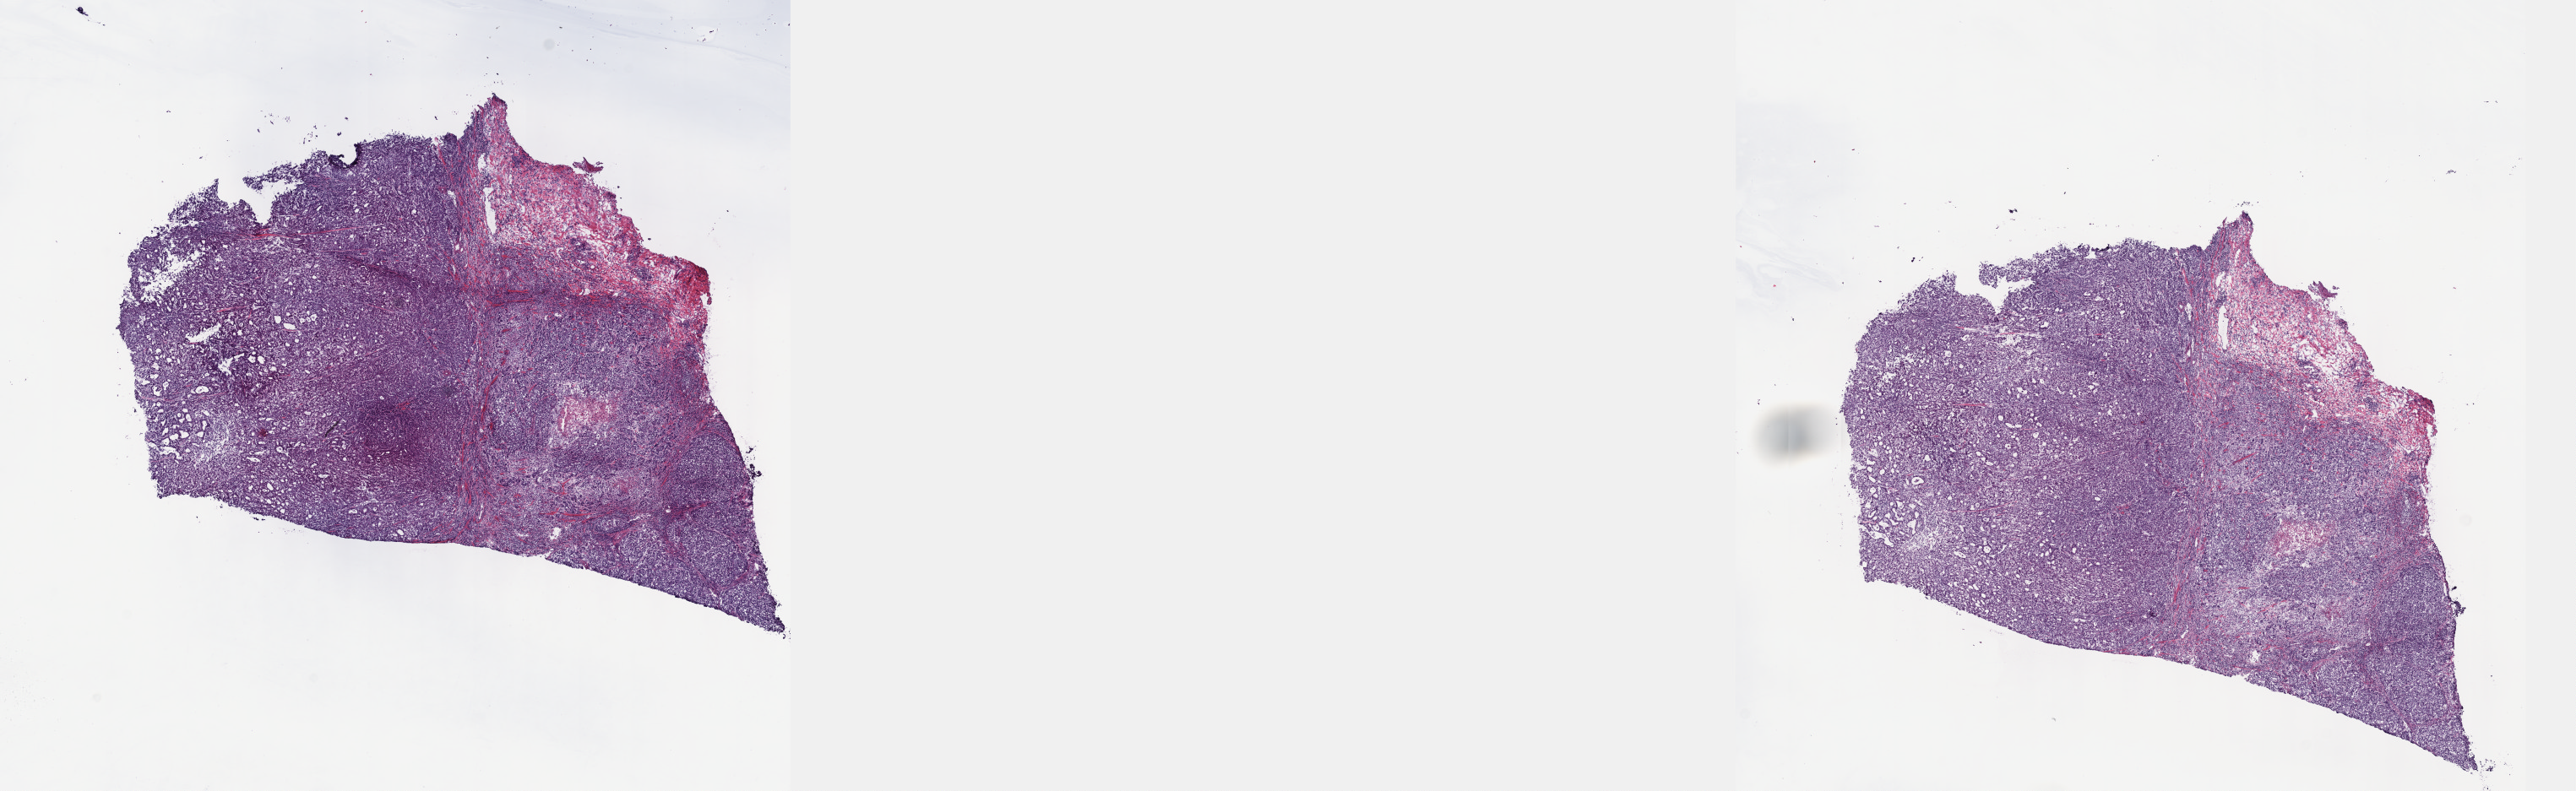
Whole-slide histology image, H&E, whole scanned area (about 24.6 x 7.6 mm, acquisition: 40x scan) shown as a low-resolution overview. Frozen section from the top of the tissue portion. Sample: primary tumour, stomach. Patient: male, age at initial diagnosis 78 years. Pathologist review of this section (percent, as recorded): tumour cells 60%, tumour nuclei 70%.
Pathologic diagnosis: Carcinoma, diffuse type (cardia, NOS).